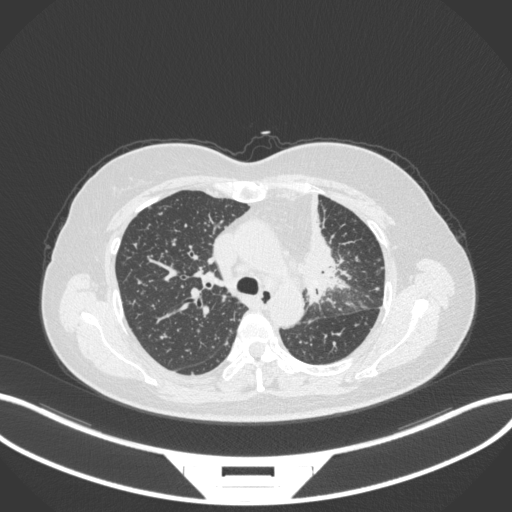
Chest CT, one axial slice; slice 229 of 348 in the series (ordered by position); reconstruction kernel B31f; 120 kVp; lung window (W 1500 / L -600 HU); 1 mm slice thickness; 512 × 512 image matrix, field of view 400 × 400 mm. Female patient, age 49 years. From the clinical record (not read from this slice): clinical TNM (as recorded): T1c N0 M1.
Annotated regions visible in this slice (bounding box drawn by a radiologist):
- lung tumour (recorded histology: adenocarcinoma): bounding box [x1, y1, x2, y2] px = [294, 193, 351, 305]